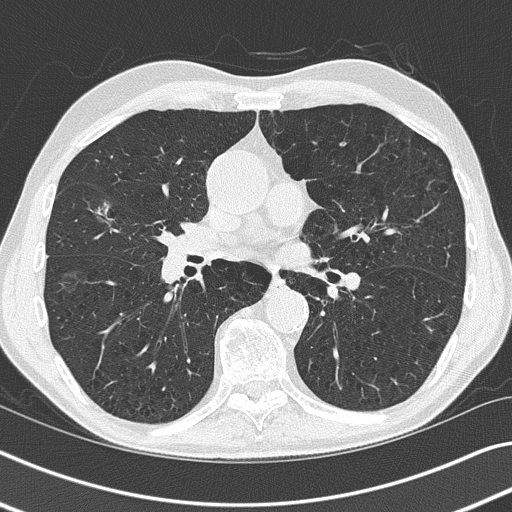
Axial slice from a low-dose chest CT screening exam, baseline annual screen, lung window (W 1500 / L -600 HU), slice 78 of 155 in the series, 512 × 512 image matrix, field of view 340 × 340 mm. Male participant, aged 73 years at enrolment. Current smoker at enrolment.
- Lesion marked by an expert reader, bounding box (x1, y1, x2, y2) in pixels: (79, 190, 131, 238).
- The screening reader recorded 3 non-calcified nodules or masses ≥4 mm on this exam; which of them this box marks is not recorded.
- Official screen result: positive, change unspecified: nodule(s) >= 4 mm or enlarging nodule(s), mass(es), or other non-specific abnormalities suspicious for lung cancer.